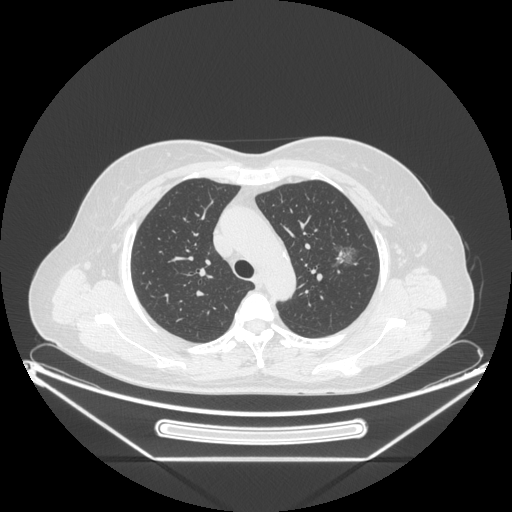
Chest CT, one axial slice; position 158 of 226 along the scan axis; lung window (W 1500 / L -600 HU); 1.25 mm slice thickness; 512 × 512 image matrix, field of view 447 × 447 mm. Female patient, age 54 years. From the clinical record (not read from this slice): clinical TNM (as recorded): T1c N0 M0; histopathological grade: G1.
Annotated regions visible in this slice (bounding box drawn by a radiologist):
- lung tumour (recorded histology: adenocarcinoma): bounding box (x1, y1, x2, y2) in pixels: (326, 243, 360, 277)